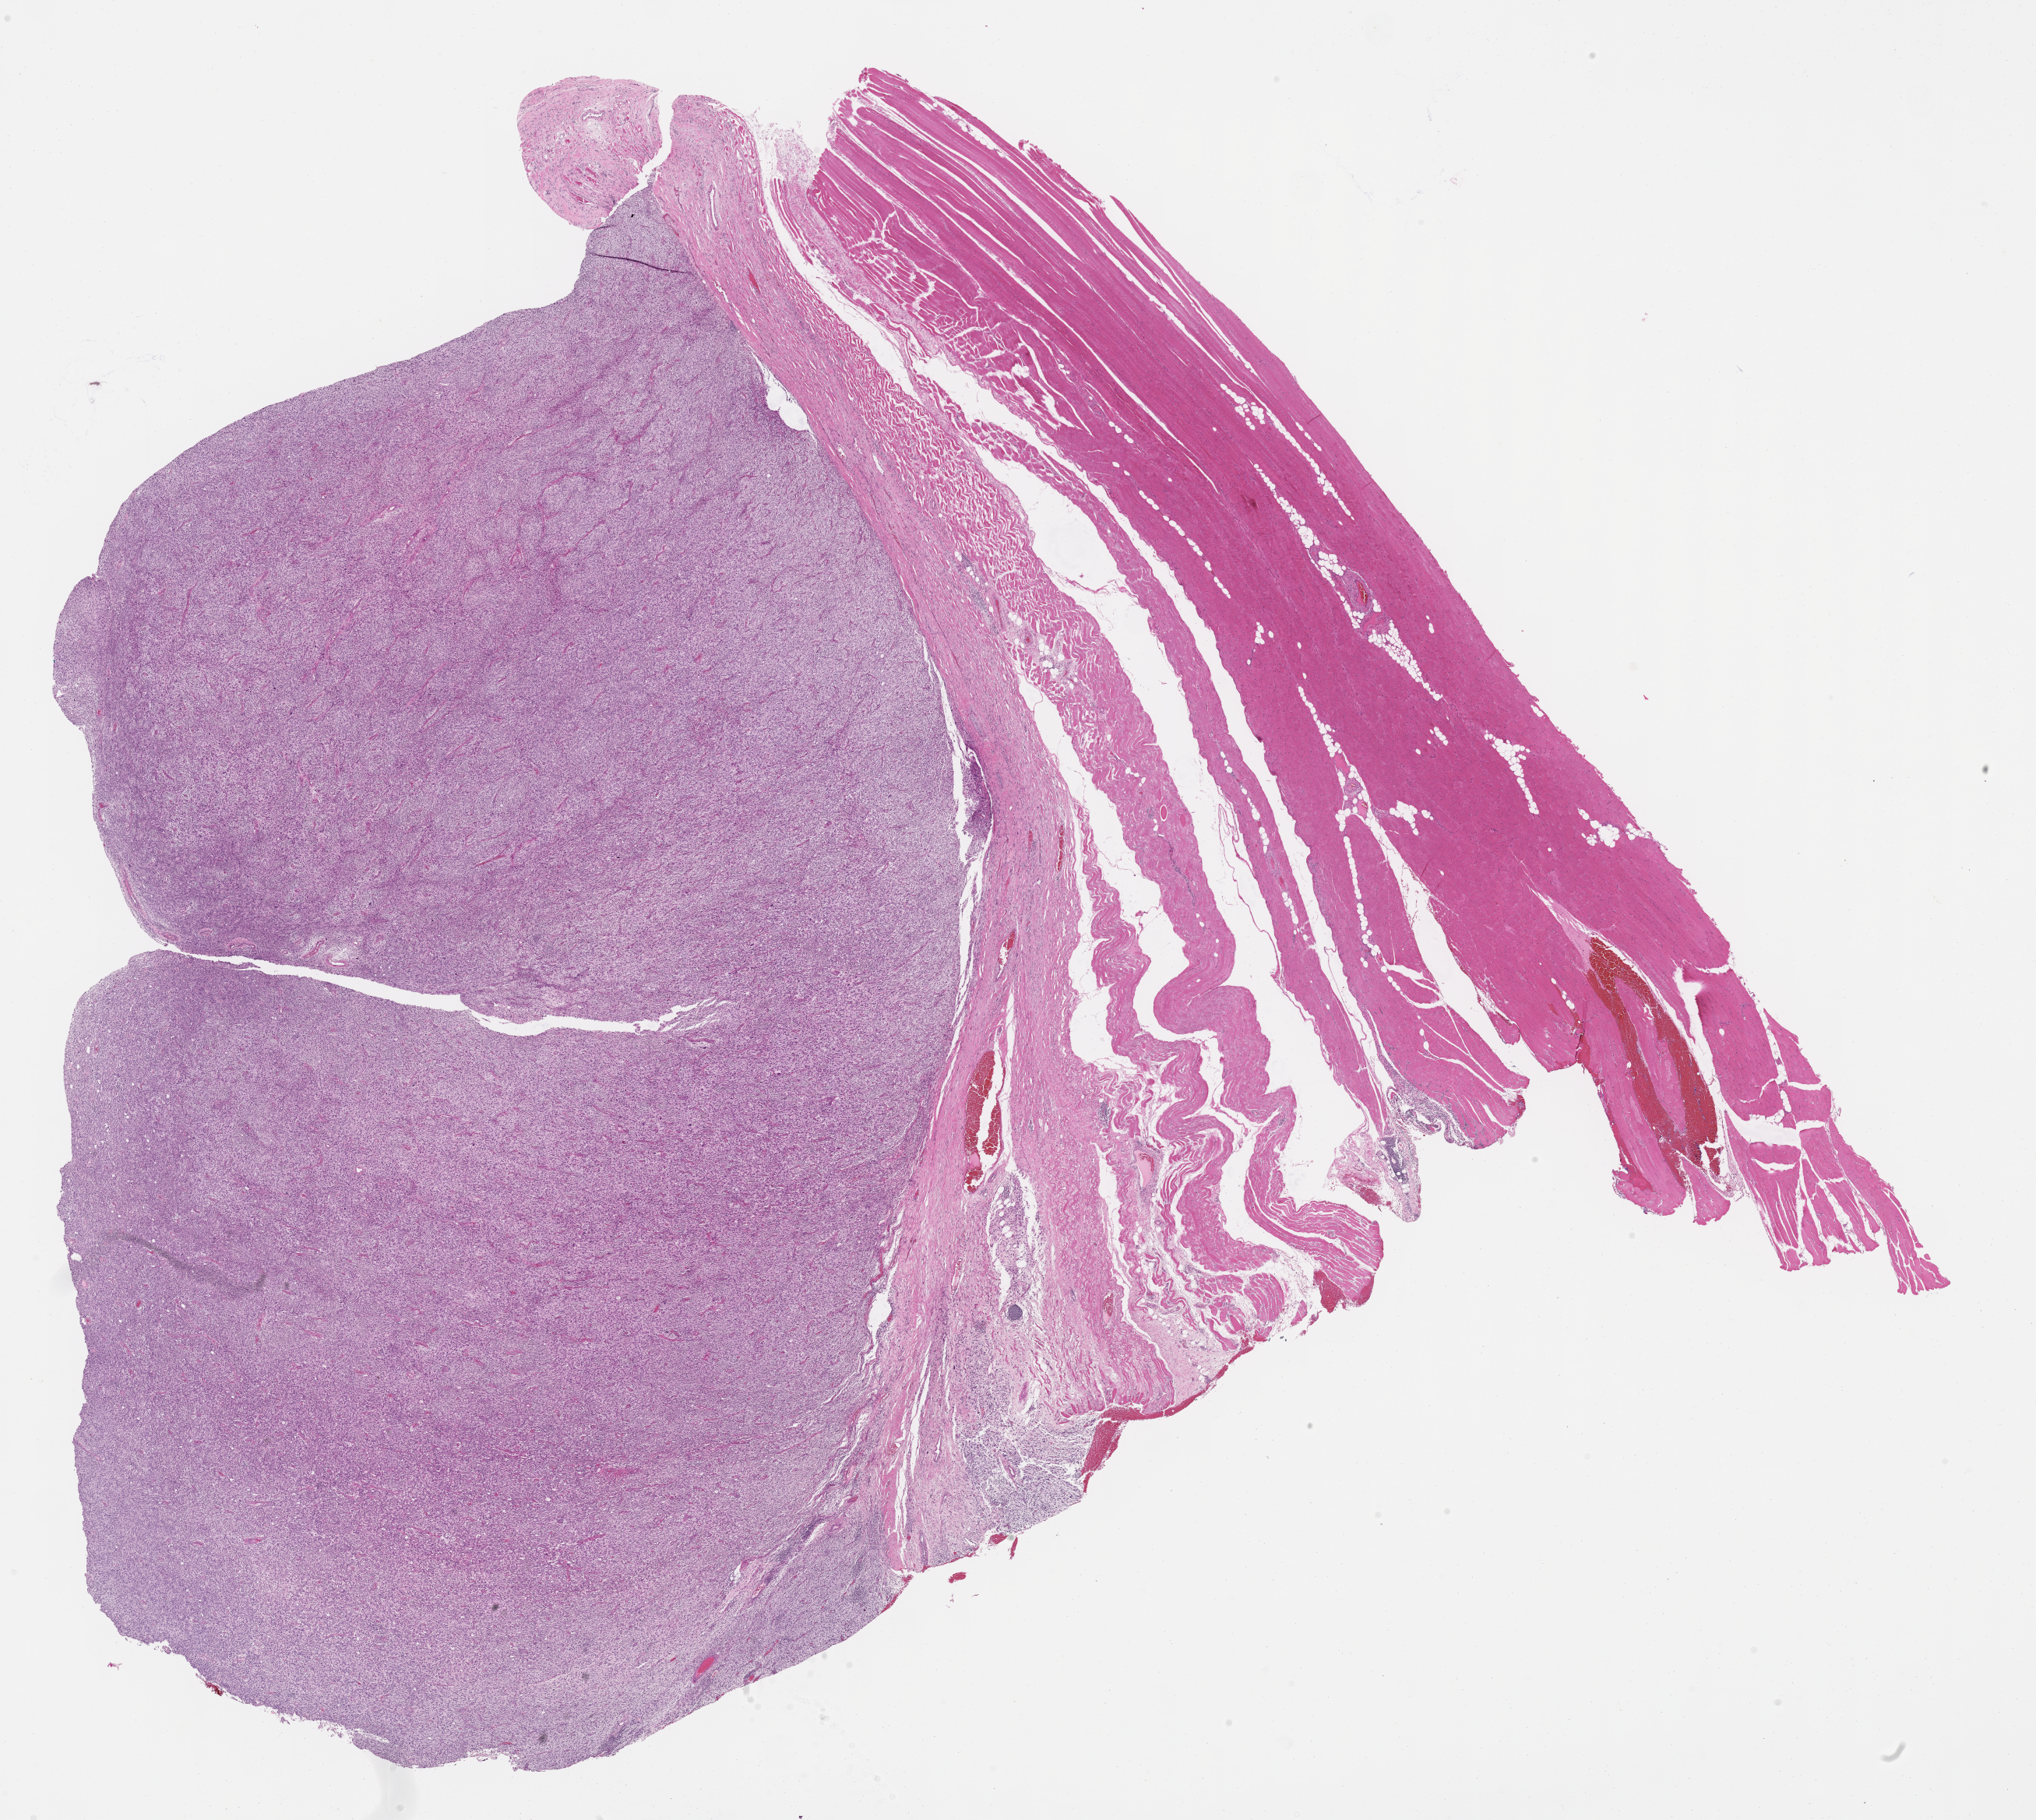
Whole-slide histology image, H&E — whole scanned area (about 21.1 x 18.9 mm, acquisition: 40x scan) shown as a low-resolution overview. FFPE section. Primary tumour sample from the connective, subcutaneous and other soft tissues. Male patient; age at initial diagnosis 61 years.
Pathologic diagnosis: Fibromyxosarcoma (connective, subcutaneous and other soft tissues of pelvis).